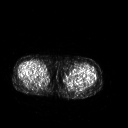
FDG PET of an extremity soft-tissue mass (from a PET/CT study), one axial slice; 3.27 mm slice thickness; 128 × 128 image matrix. Patient: female, 42 years. Case-level facts recorded for this patient, not image findings: histological type: pleiomorphic leiomyosarcoma; grade: intermediate; site of the primary tumour: left thigh.
Structures marked on this image (expert contour drawn on MRI and transferred to this co-registered scan by the dataset authors):
- gross tumour volume including surrounding oedema: box from (x=78, y=77) to (x=80, y=79) px